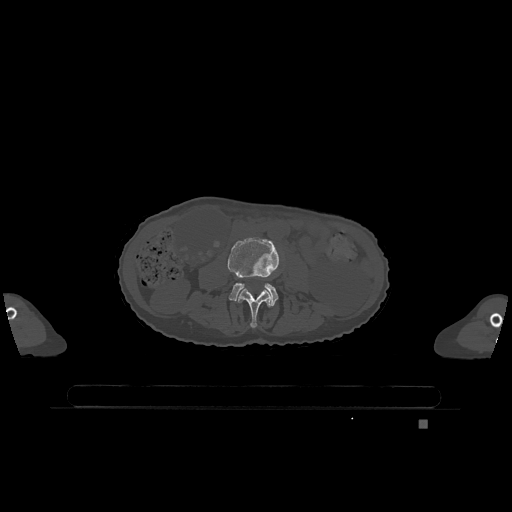
CT including the spine, one axial slice. Slice 329 of 1317 in the series (ordered by position). Bone window (W 1800 / L 400 HU). 0.5 mm slice thickness. 512 × 512 image matrix, field of view 500 × 500 mm. Patient: female, 74 years. From the clinical record (not read from this slice): primary cancer: lung; vertebrae with lytic lesions (as recorded): T1, T4, T5, T6, L4, L5.
Annotated regions visible in this slice (semi-automatically segmented with operator editing):
- L3 vertebra: bounding box [x1, y1, x2, y2] px = [238, 288, 272, 328]
- L4 vertebra: [227, 236, 279, 305]